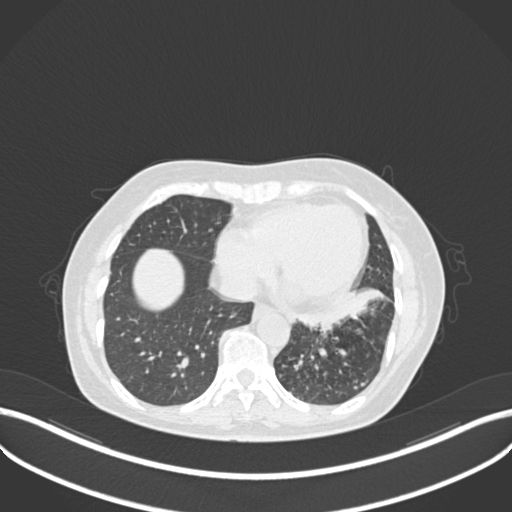
Chest CT, one axial slice. Slice 84 of 270 in the series (ordered by position). 120 kVp. Lung window (W 1500 / L -600 HU). 1 mm slice thickness. 512 × 512 image matrix, field of view 400 × 400 mm. Female patient, age 63 years. Case-level facts recorded for this patient, not image findings: clinical TNM (as recorded): T1b N0 M0; histopathological grade: G2-3.
Structures marked on this image (bounding box drawn by a radiologist):
- lung tumour (recorded histology: adenocarcinoma): bounding box [x1, y1, x2, y2] px = [293, 290, 386, 330]